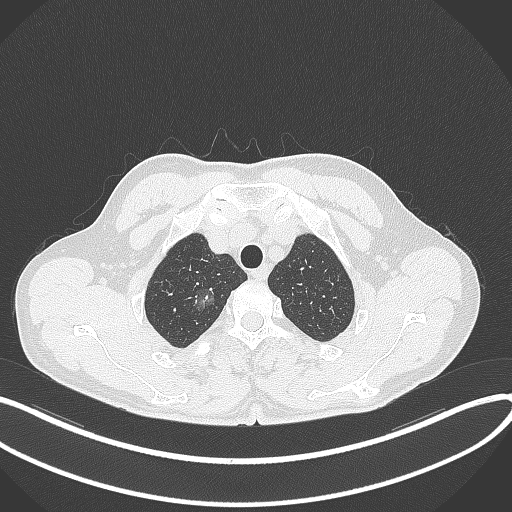
Chest CT, one axial slice. Reconstruction kernel B70f. 120 kVp. Lung window (W 1500 / L -600 HU). 1 mm slice thickness. 512 × 512 image matrix, field of view 400 × 400 mm. Male patient, age 58 years. Case-level facts recorded for this patient, not image findings: clinical TNM (as recorded): T1c N0 M0; histopathological grade: G1-2.
Structures marked on this image (bounding box drawn by a radiologist):
- lung tumour (recorded histology: adenocarcinoma): bounding box <182,280,222,318> (left, top, right, bottom; pixels)